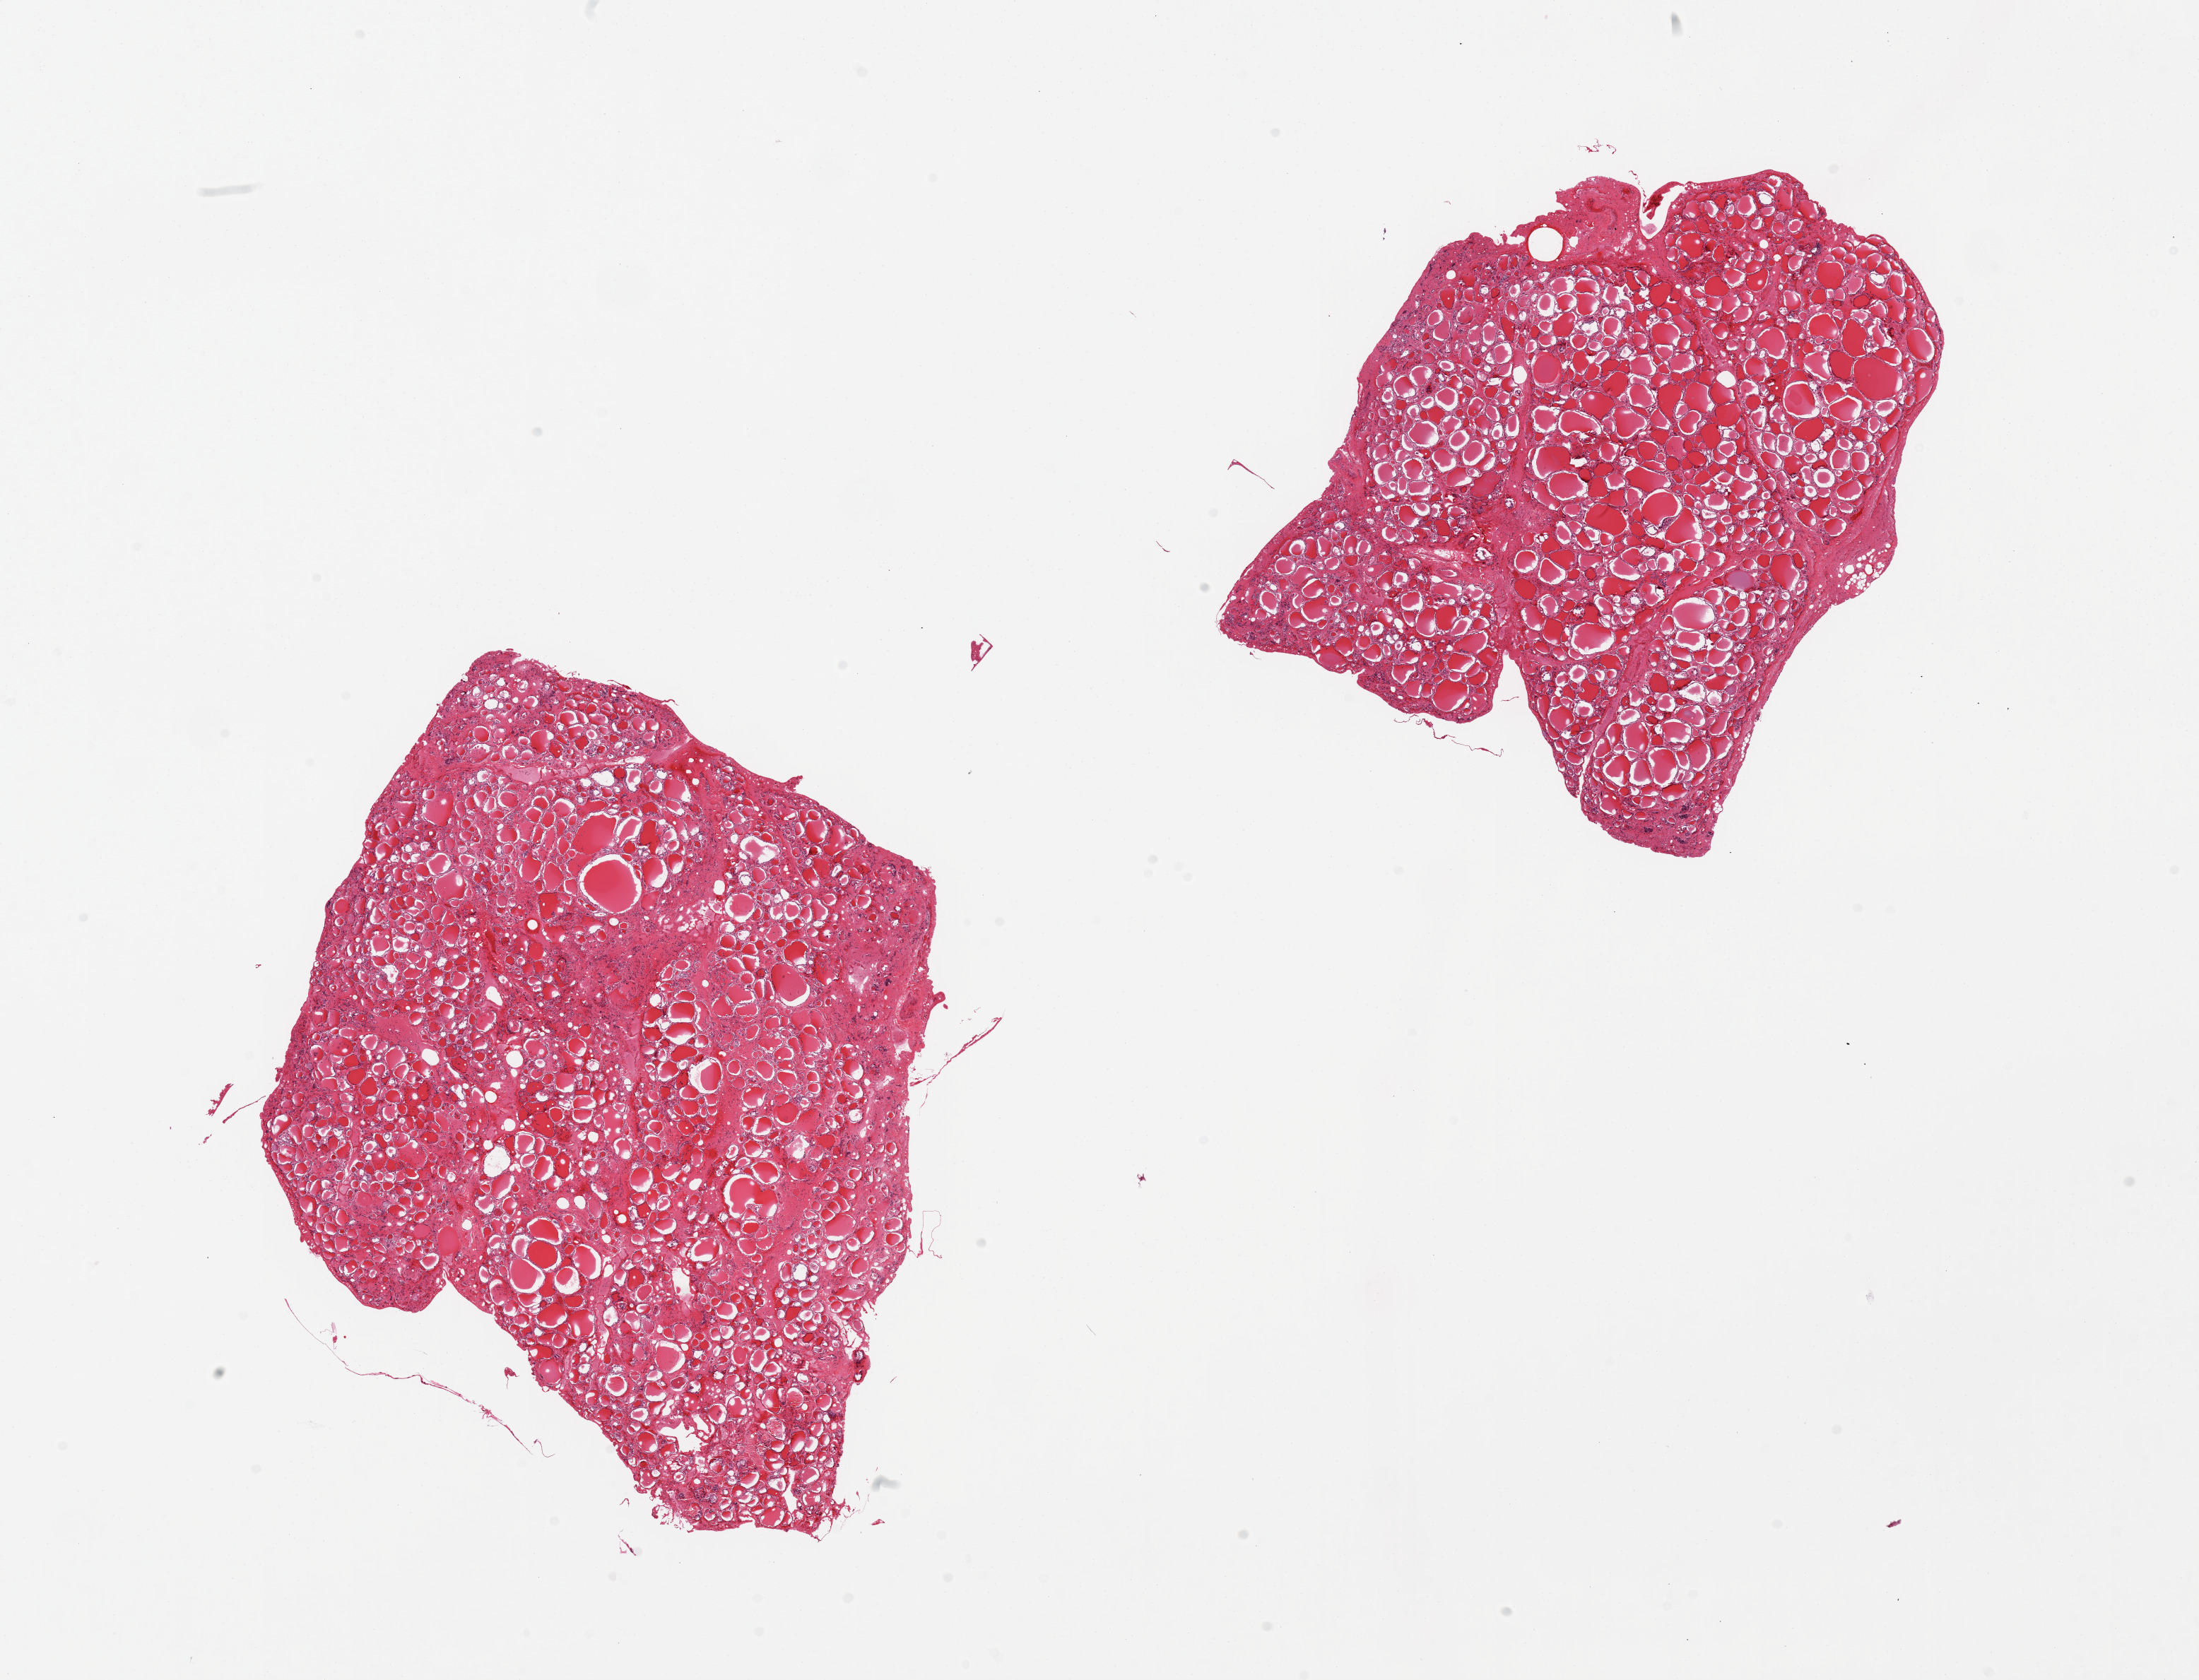
H&E whole-slide image — a low-resolution overview of the entire scanned area, about 24.6 x 18.8 mm (acquisition: 20x scan); PAXgene-fixed, paraffin-embedded tissue; target tissue: thyroid; tissue donor sample. Male donor.
• pathologist's review note for this sample: 2 pieces, moderatedly autolyzed, regressive changes